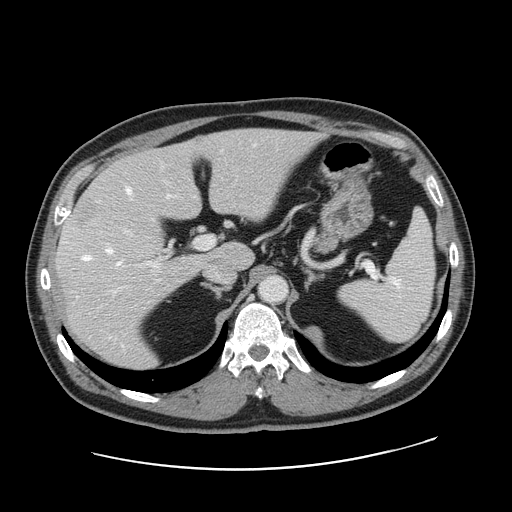
Contrast-enhanced abdominal CT, one axial slice. Slice 106 of 178 in the series (ordered by position). 120 kVp. Intravenous contrast given. Soft-tissue window (W 400 / L 40 HU). 2.5 mm slice thickness. 512 × 512 image matrix, field of view 403 × 403 mm. Male patient, age 63 years. From the clinical record (not read from this slice): diagnosis: colorectal cancer liver metastases, imaged before liver resection; multiple liver metastases: yes; largest metastasis: 8 cm.
Structures marked on this image (manually delineated by an expert):
- hepatic veins: bounding box <83,187,169,264> (left, top, right, bottom; pixels)
- liver: <57,128,316,369>
- planned liver remnant (the part of the liver to remain after resection): <126,128,314,269>
- portal vein (with intrahepatic branches): <124,230,215,266>
- liver metastasis: <72,198,98,229>